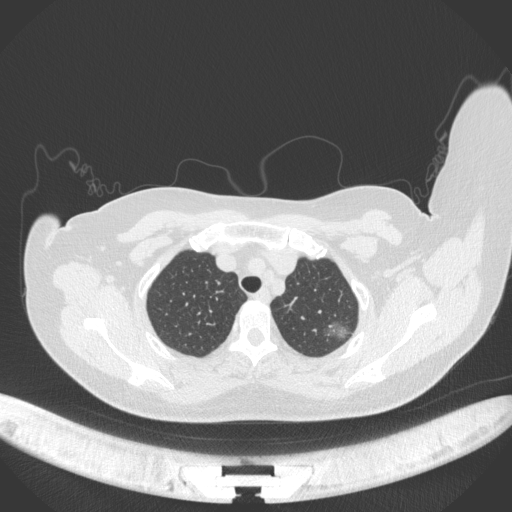
Chest CT, one axial slice; slice 310 of 386 in the series (ordered by position); 120 kVp; lung window (W 1500 / L -600 HU); 1 mm slice thickness; 512 × 512 image matrix, field of view 400 × 400 mm. Patient: female, 58 years. From the clinical record (not read from this slice): clinical TNM (as recorded): T1c N0 M0.
Outlined on this slice (bounding box drawn by a radiologist):
- lung tumour (recorded histology: adenocarcinoma): bounding box (x1, y1, x2, y2) in pixels: (325, 321, 352, 342)